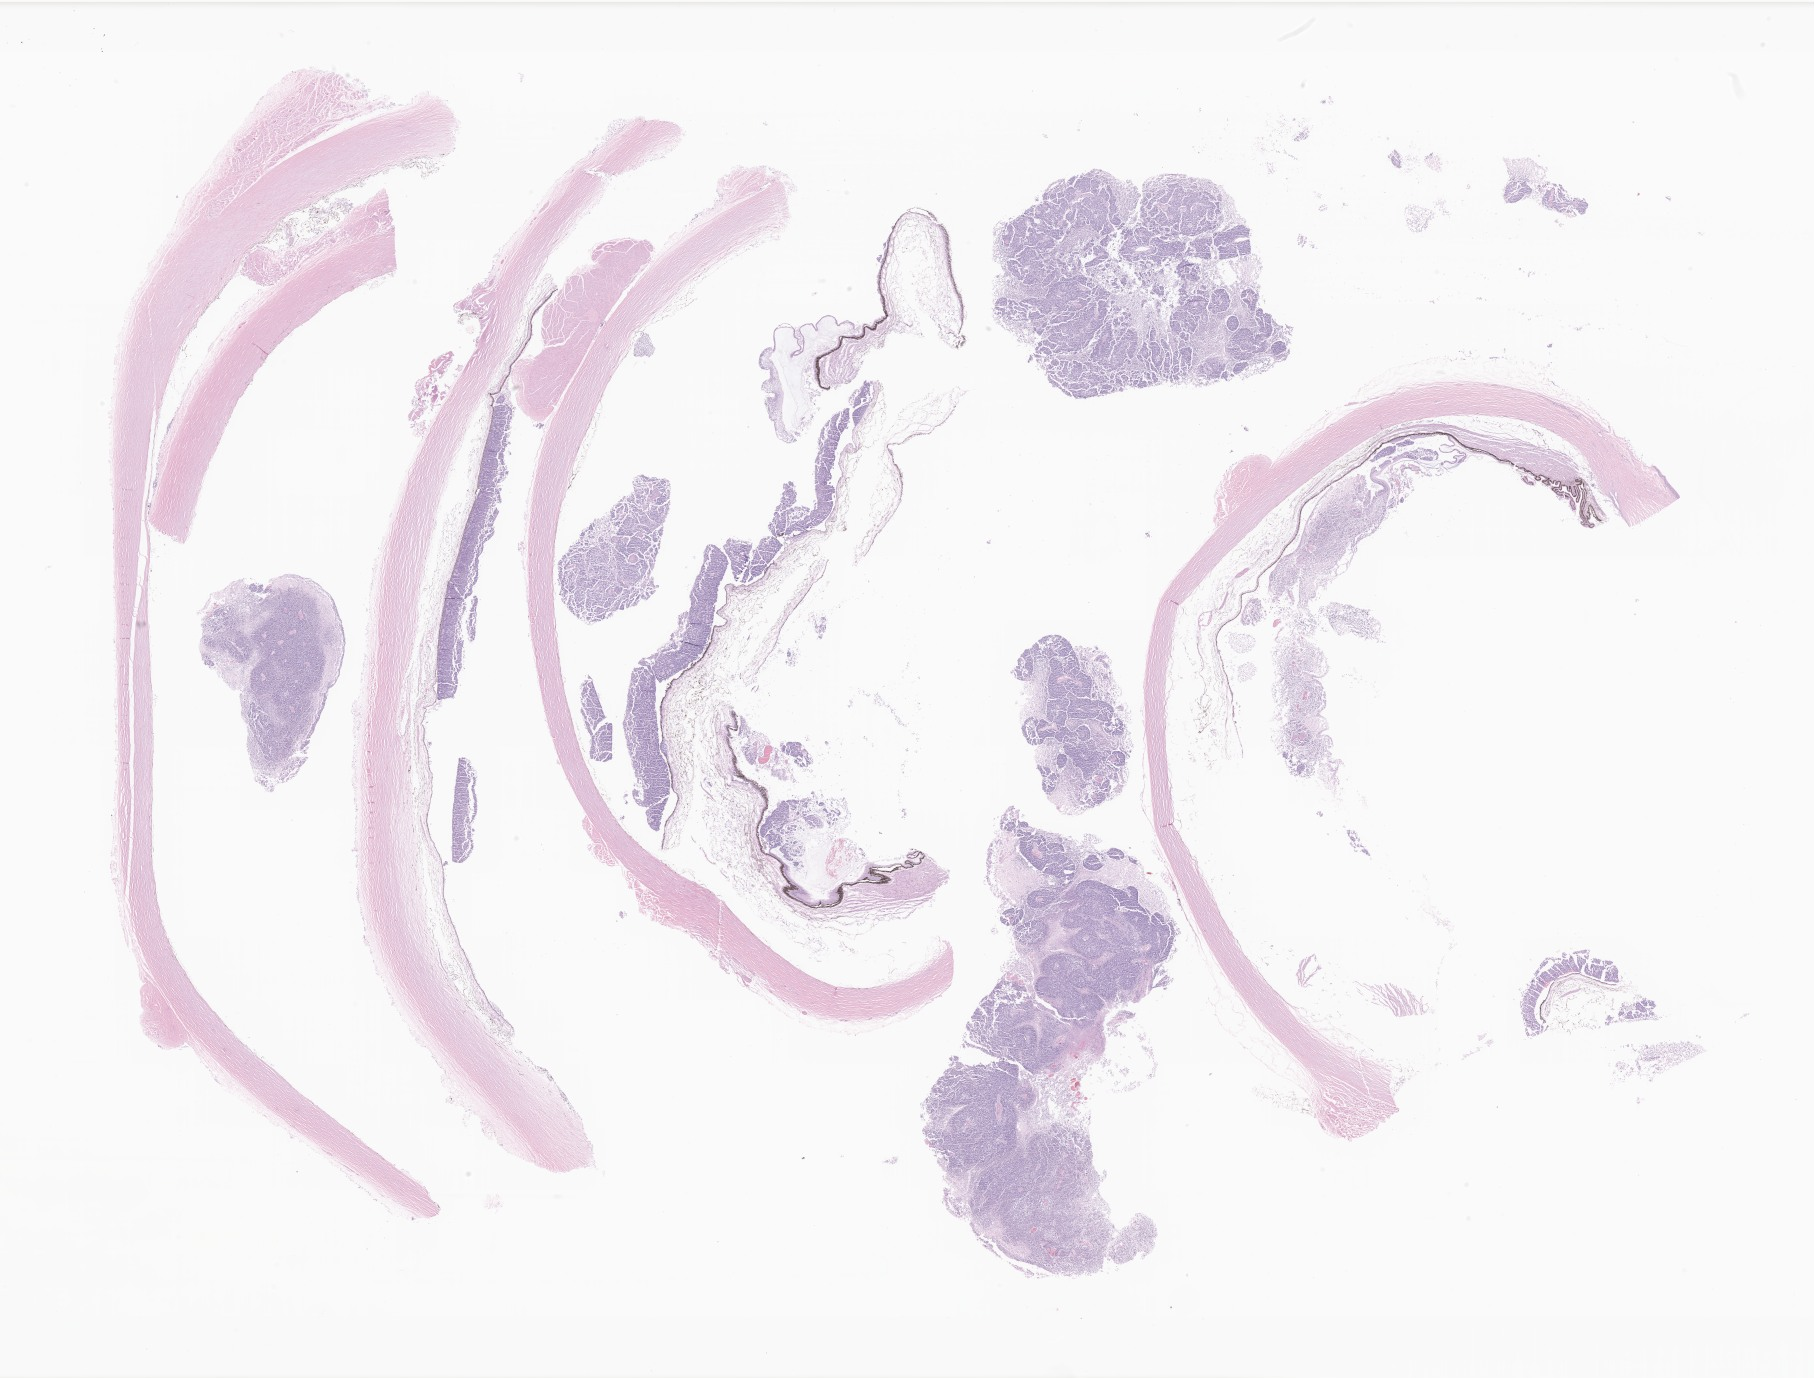
Whole-slide image, haematoxylin and eosin stain of tumor tissue from the retina — whole scanned area (about 30.6 x 23.2 mm) shown as a low-resolution overview; formalin-fixed, paraffin-embedded (FFPE) tissue. Patient male; age 35 months (2 years 11 months).
* diagnosis (ICD-O-3 morphology term): Retinoblastoma, NOS